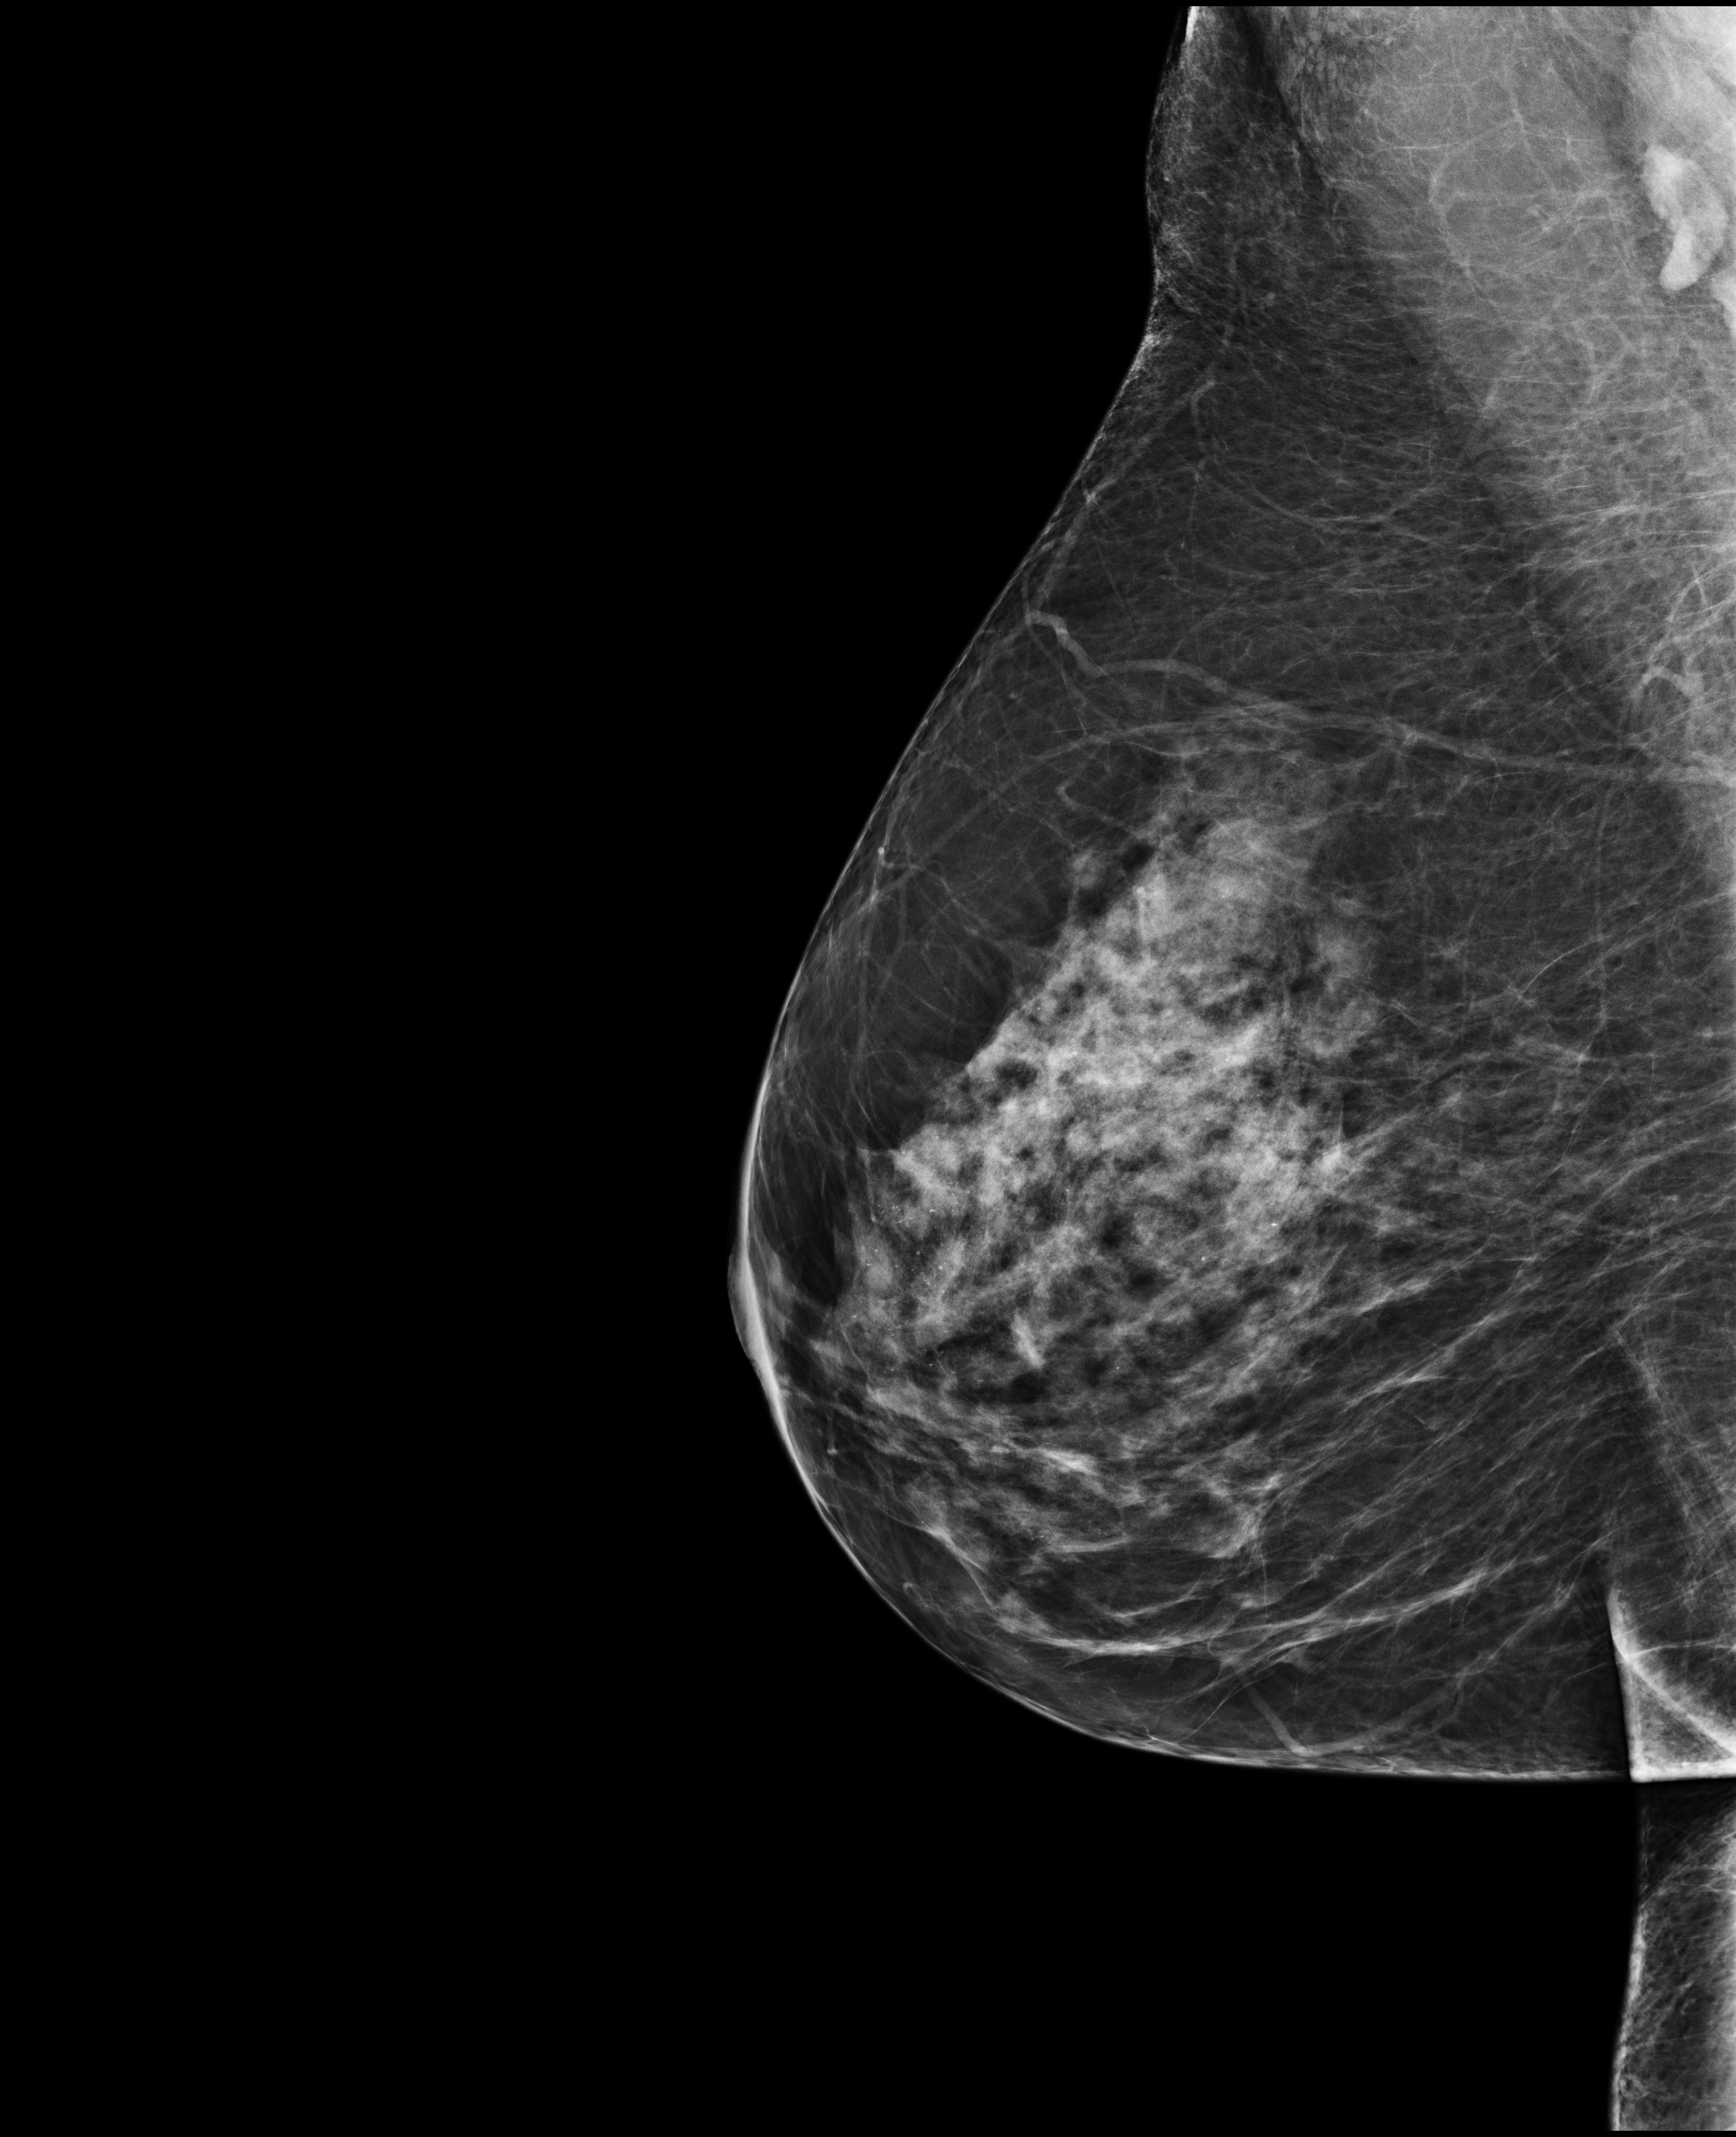
Annual screening mammography examination; system: Selenia Dimensions.
Image type: full-field digital mammogram. Breast: right. Projection: mediolateral oblique (MLO) view.